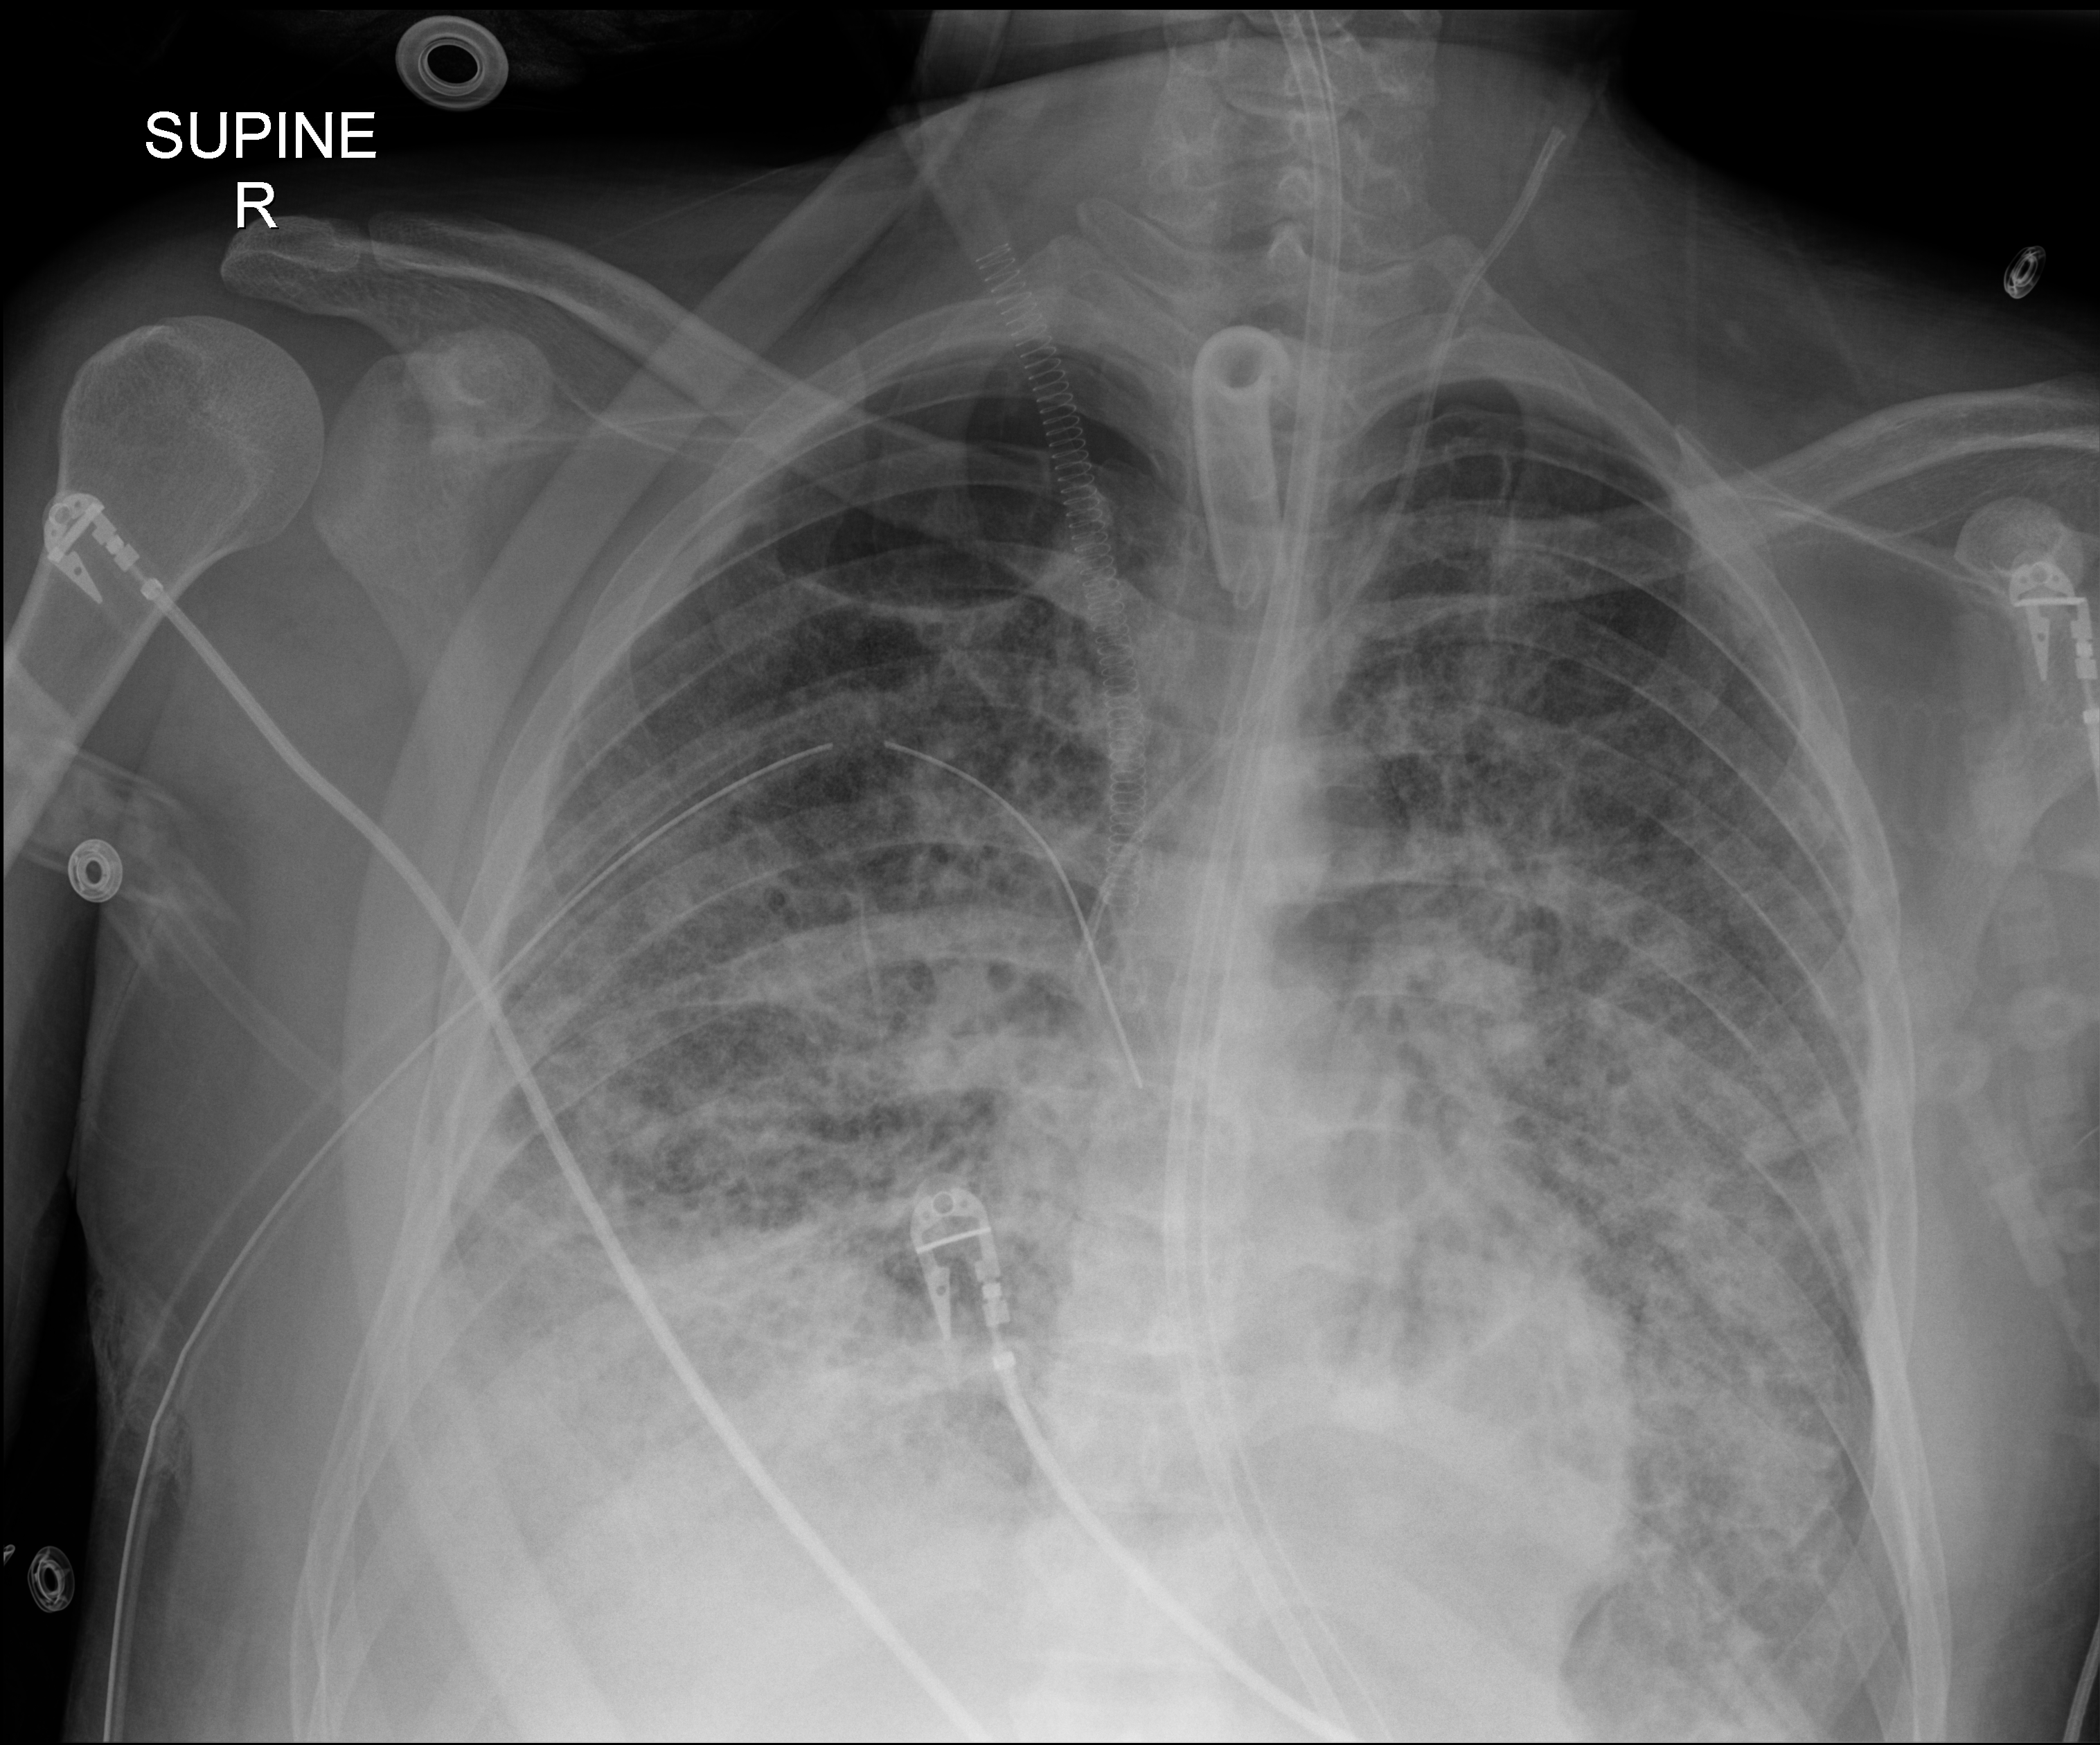
Chest radiograph. Patient hospitalised with COVID-19, aged 18–59 years.
From the hospital-stay record, not from the radiograph (when in the stay this image was taken is not recorded):
- mechanically ventilated during this hospital stay: yes
- other chronic lung disease (admission record): no
- length of hospital stay: 60 days